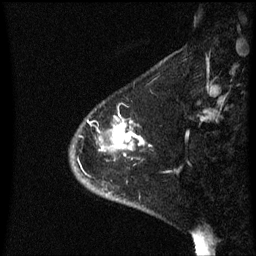
Breast MRI (dynamic contrast-enhanced), one sagittal slice; slice 16 of 60 in the series (ordered by position); dynamic contrast-enhanced series, image 2 of 3 at this slice position (ordered by acquisition); 1.5 T; TE 4.2 ms, TR 8.4 ms; 256 × 256 image matrix, field of view 200 × 200 mm. Female patient, age 46 years. From the clinical record (not read from this slice): setting: breast cancer imaged before/during neoadjuvant chemotherapy; receptor status: HER2-positive.
Structures marked on this image (semi-automatic segmentation, software-assisted and operator-edited):
- analysis volume of interest (the breast-tissue region the enhancement analysis was run in; not a lesion): bounding box <70,116,145,187> (left, top, right, bottom; pixels)
- tumour enhancement mask (voxels above the 70 % enhancement threshold inside the analysis volume of interest): <100,116,144,157>